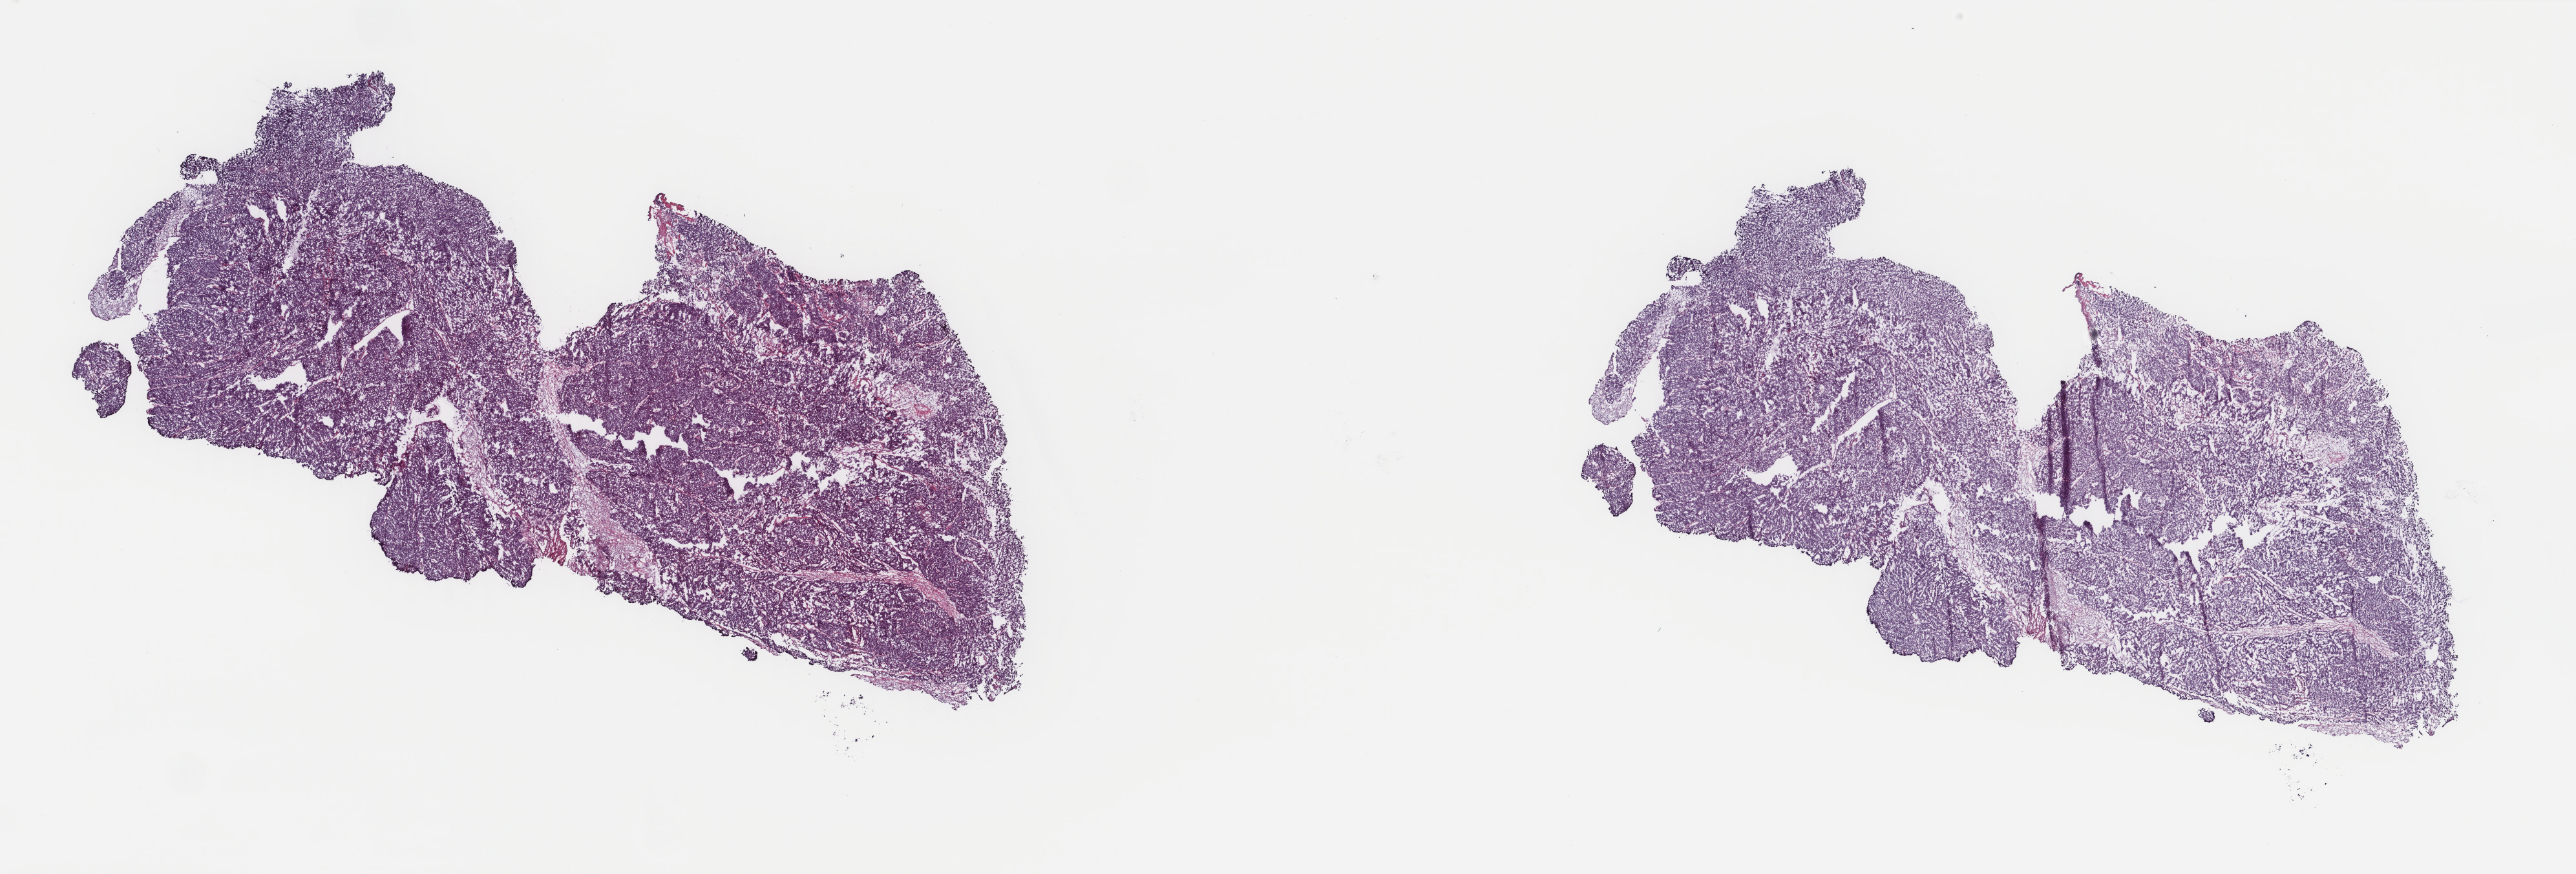
Hematoxylin and eosin (H&E) stained whole-slide image, a low-resolution overview of the entire scanned area, about 31.6 x 10.7 mm. Frozen section from the top of the tissue portion. Primary tumour sample from the uterus. Female, age 82 years at initial diagnosis. Histologic grade: G3 (poorly differentiated). Slide review estimates, as recorded: tumour cells 100%, tumour nuclei 90%, normal cells 0%, stromal cells 0%, necrosis 0%. Infiltration values recorded for this section: lymphocyte infiltration 2%, monocyte infiltration 0%, neutrophil infiltration 0%.
FIGO stage: IA. Diagnosis: Endometrioid adenocarcinoma, NOS.